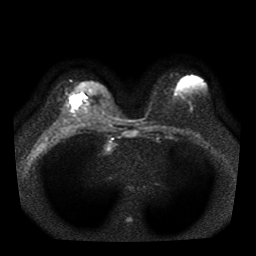
Breast MRI, one axial slice; position 24 of 41 along the scan axis; diffusion-weighted series; image 2 of 4 stored at this slice position (different b-values; order by instance number); 1.5 T; 5 mm slice thickness; 256 × 256 image matrix. Female patient.
Structures marked on this image (outlined manually by an expert reader):
- tumour on diffusion-weighted imaging: bounding box <69,95,82,109> (left, top, right, bottom; pixels)